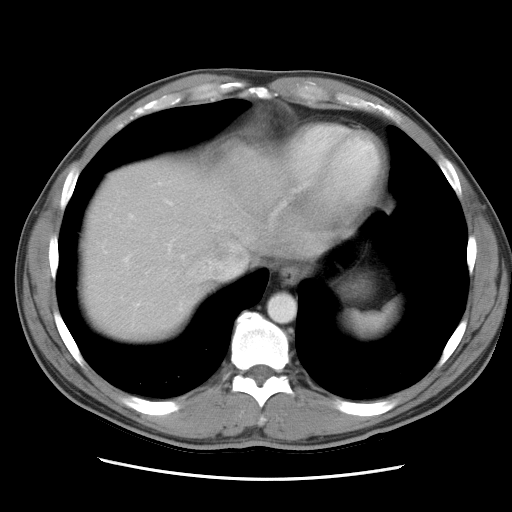
Contrast-enhanced abdominal CT, one axial slice. Position 26 of 34 along the scan axis. Intravenous contrast given. Soft-tissue window (W 400 / L 40 HU). 7.5 mm slice thickness. 512 × 512 image matrix. Male patient, age 40 years. Case-level facts recorded for this patient, not image findings: diagnosis: colorectal cancer liver metastases, imaged before liver resection.
Structures marked on this image (manually delineated by an expert):
- hepatic veins: box from (x=163, y=261) to (x=242, y=278) px
- liver: (x=79, y=155)–(x=269, y=341)
- planned liver remnant (the part of the liver to remain after resection): (x=79, y=154)–(x=271, y=343)
- portal vein (with intrahepatic branches): (x=124, y=184)–(x=184, y=309)